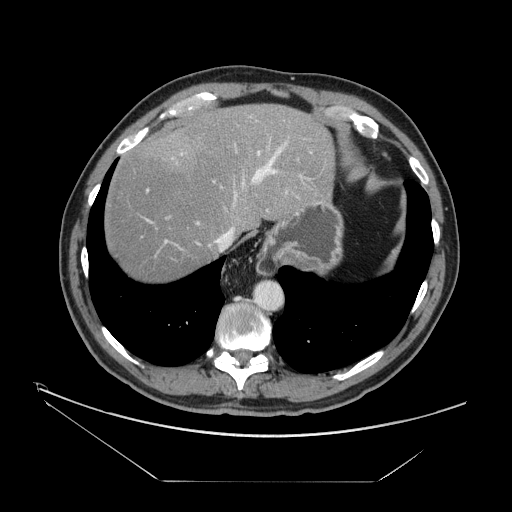
Contrast-enhanced abdominal CT, one axial slice. Slice 131 of 161 in the series (ordered by position). Reconstruction kernel STANDARD. 120 kVp. Intravenous contrast given. Soft-tissue window (W 400 / L 40 HU). 2.5 mm slice thickness. 512 × 512 image matrix, field of view 440 × 440 mm. Male patient, age 65 years. Case-level facts recorded for this patient, not image findings: diagnosis: colorectal cancer liver metastases, imaged before liver resection; multiple liver metastases: yes; largest metastasis: 4.2 cm; disease in both lobes: yes.
Structures marked on this image (manually delineated by an expert):
- hepatic veins: box from (x=208, y=143) to (x=286, y=252) px
- liver: (x=104, y=104)–(x=333, y=282)
- planned liver remnant (the part of the liver to remain after resection): (x=104, y=104)–(x=333, y=283)
- portal vein (with intrahepatic branches): (x=146, y=114)–(x=302, y=248)